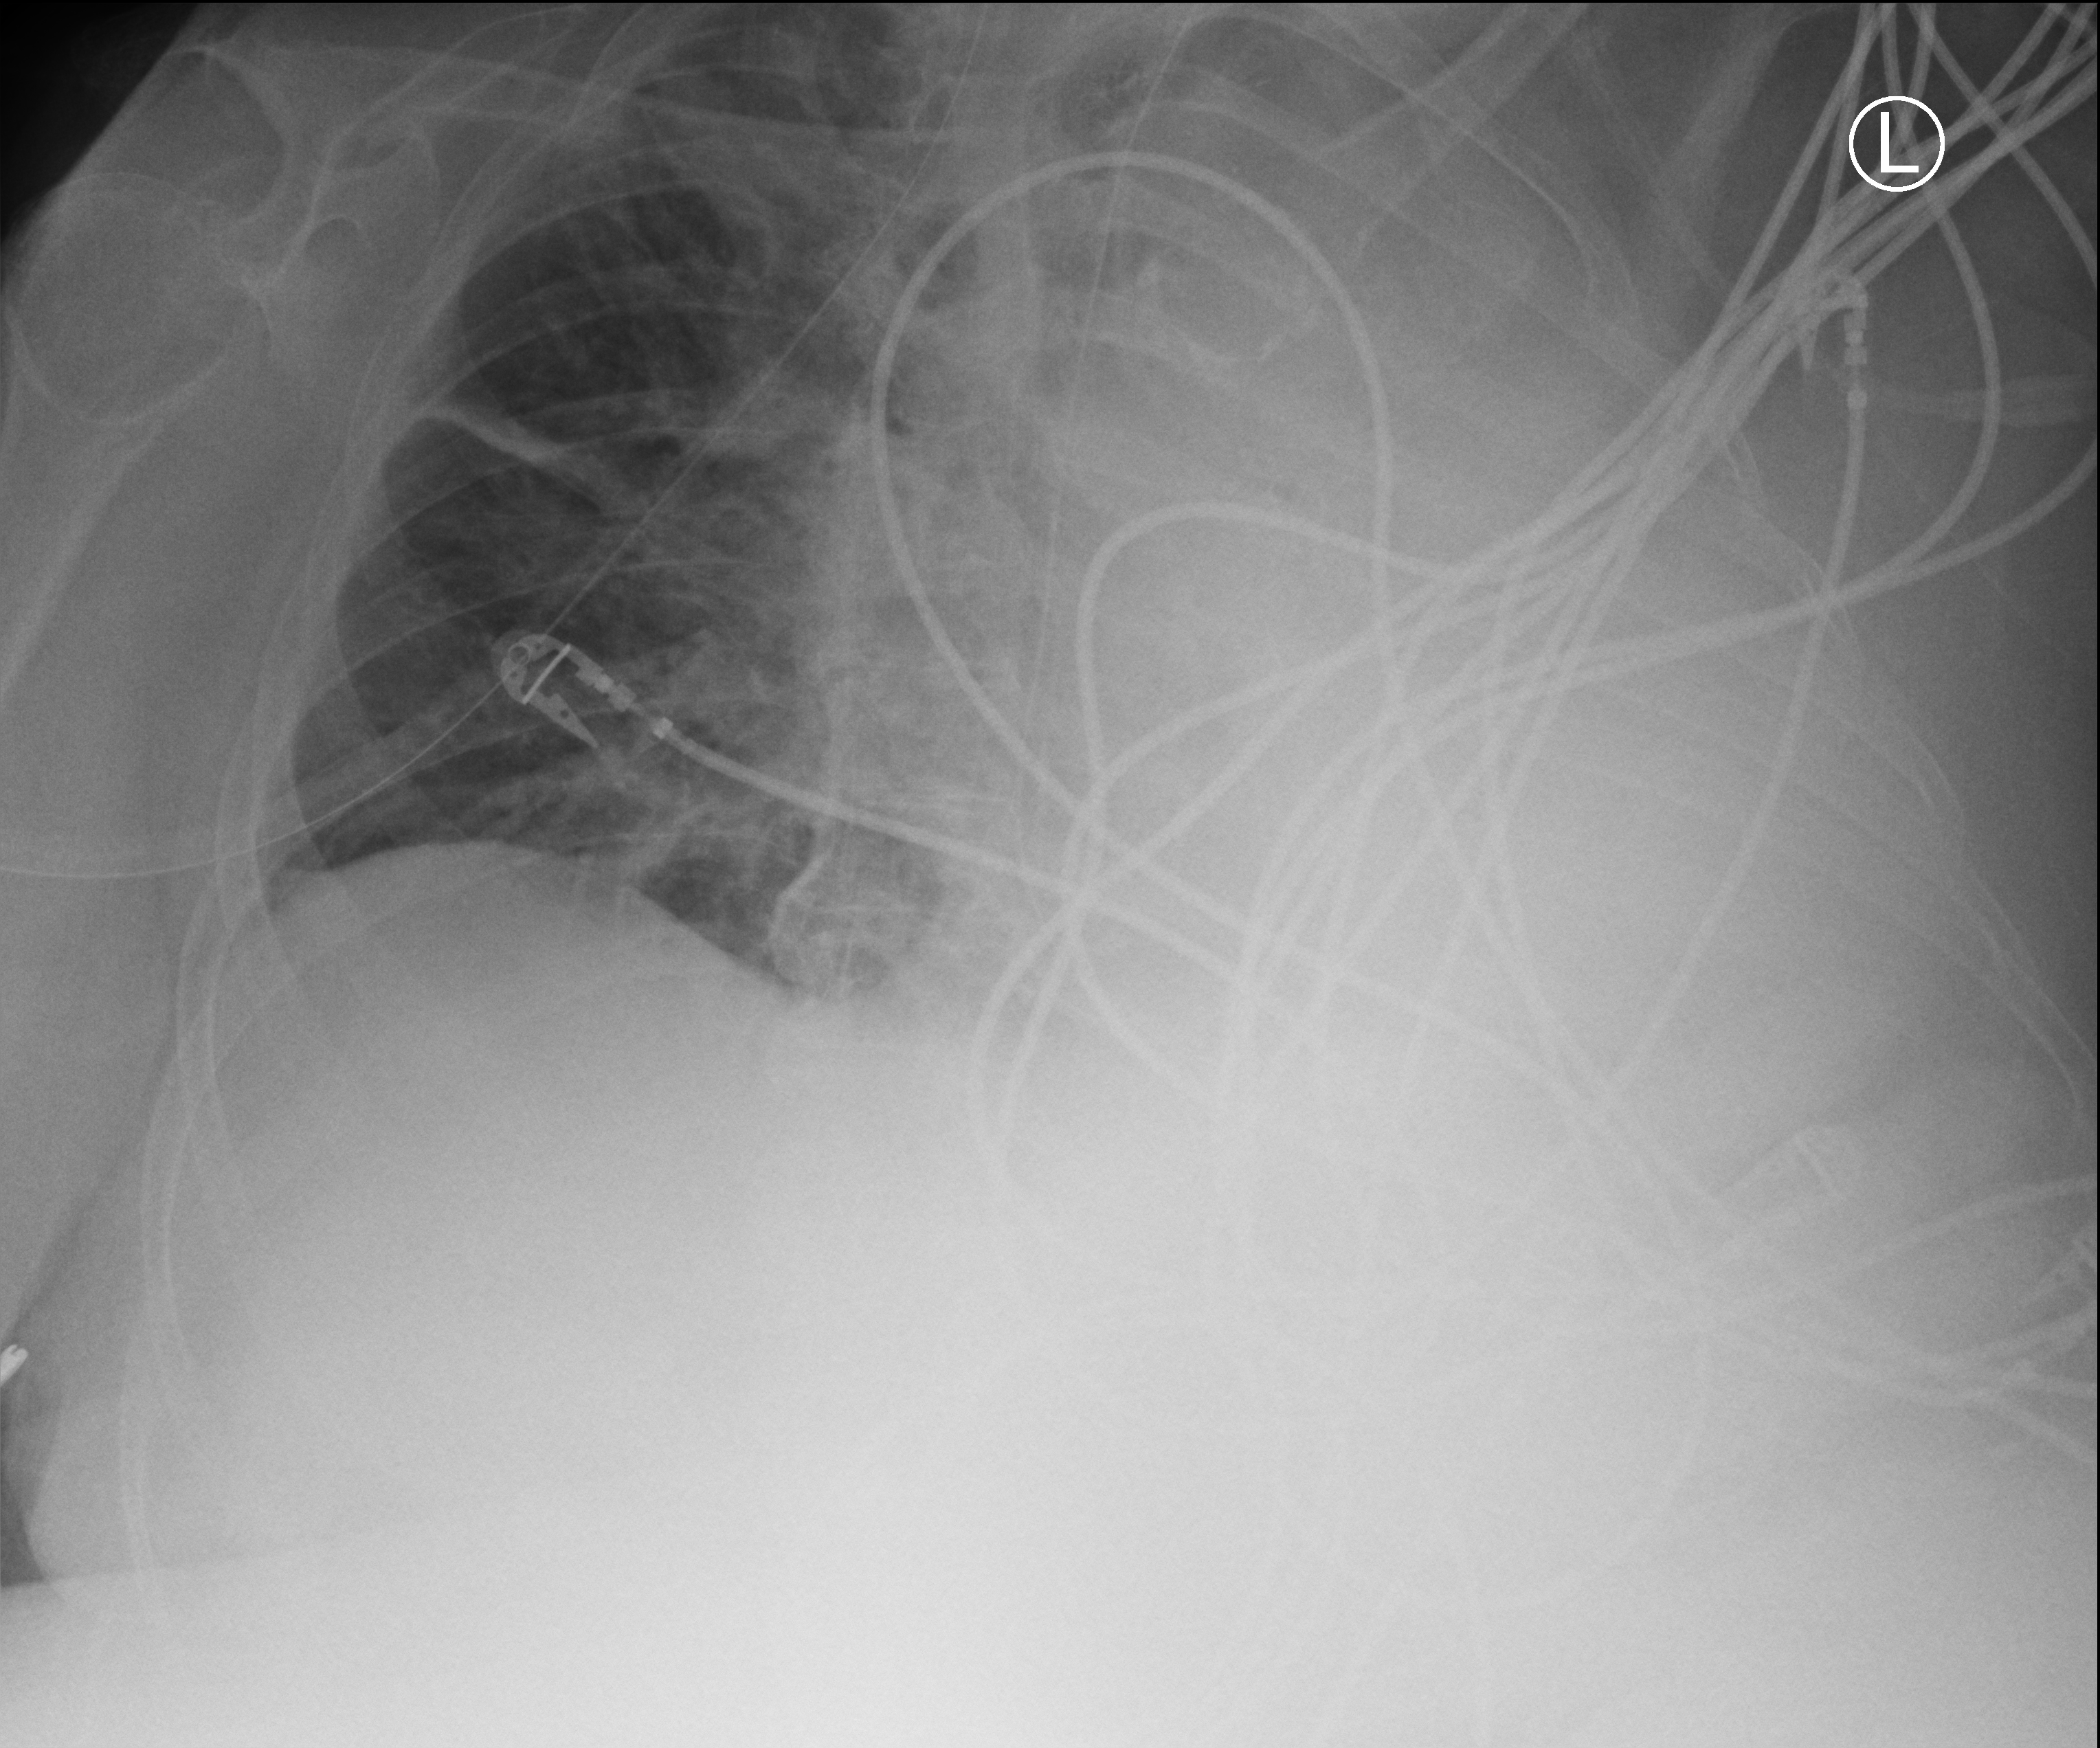
Bedside chest radiograph (computed radiography); anteroposterior (AP) projection. Female patient hospitalised with COVID-19, age 75–90 years.
Admission-level facts for this patient (not findings on this image; timing relative to this image not recorded): length of hospital stay: 5 days; mechanically ventilated during this hospital stay: no.